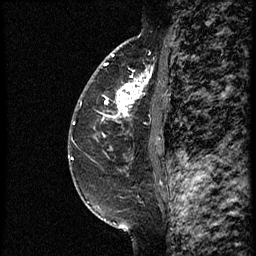
Breast MRI (dynamic contrast-enhanced), one sagittal slice. Slice 40 of 60 in the series (ordered by position). Dynamic contrast-enhanced study with each time point stored as its own series, time point 2 of 3 at this slice position (early post-contrast, ordered by acquisition time). 1.5 T. TE 4.2 ms, TR 18.9 ms. 2 mm slice thickness. 256 × 256 image matrix. Female patient. From the clinical record (not read from this slice): setting: breast cancer imaged before/during neoadjuvant chemotherapy; receptor status: HER2-positive.
Structures marked on this image (semi-automatic segmentation, software-assisted and operator-edited):
- analysis volume of interest (the breast-tissue region the enhancement analysis was run in; not a lesion): bounding box (x1, y1, x2, y2) in pixels: (93, 64, 161, 147)
- tumour enhancement mask (voxels above the 100 % enhancement threshold inside the analysis volume of interest): (108, 71, 161, 141)